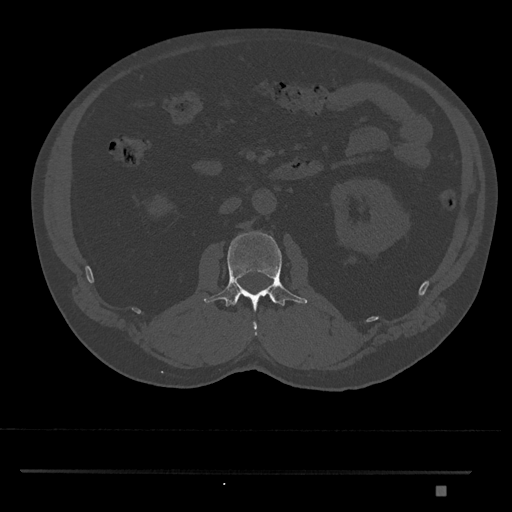
CT including the spine, one axial slice. Position 756 of 1134 along the scan axis. Reconstruction kernel Br40s/3. Bone window (W 1800 / L 400 HU). 0.5 mm slice thickness. 512 × 512 image matrix, field of view 429 × 429 mm. Patient: male, 65 years. From the clinical record (not read from this slice): primary cancer: prostate.
Annotated regions visible in this slice (semi-automatically segmented with operator editing):
- L2 vertebra: box from (x=204, y=231) to (x=307, y=335) px